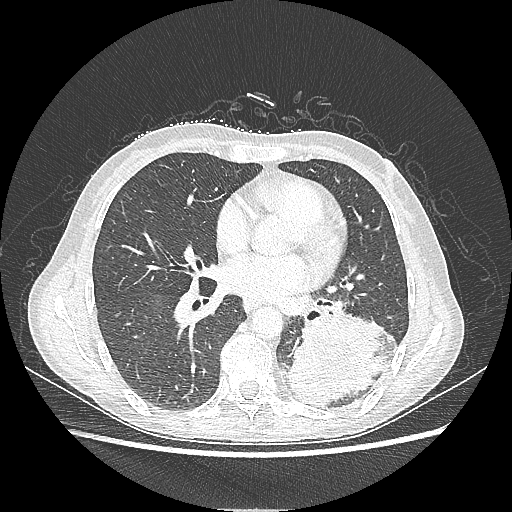
Chest CT, one axial slice. Slice 105 of 220 in the series (ordered by position). Reconstruction kernel LUNG. Lung window (W 1500 / L -600 HU). 1.25 mm slice thickness. 512 × 512 image matrix, field of view 360 × 360 mm. Female patient, age 53 years. From the clinical record (not read from this slice): clinical TNM (as recorded): T3 N0 M0.
Structures marked on this image (rectangle marked by the reading radiologist):
- lung tumour (recorded histology: adenocarcinoma): box from (x=288, y=311) to (x=398, y=408) px